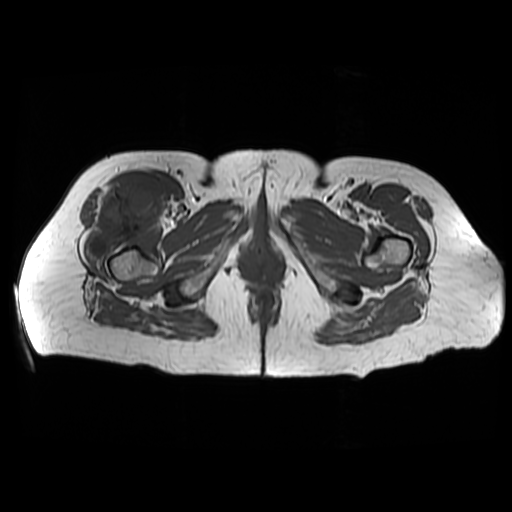
MRI of an extremity soft-tissue mass, one axial slice. Position 38 of 48 along the scan axis. 512 × 512 image matrix. Female patient. From the clinical record (not read from this slice): histological type: pleiomorphic undifferentiated sarcoma; grade: high; site of the primary tumour: right quadricep.
Structures marked on this image (expert manual segmentation):
- gross tumour volume including surrounding oedema: bounding box (x1, y1, x2, y2) in pixels: (87, 180, 162, 258)
- gross tumour volume (mass): (87, 180, 162, 258)